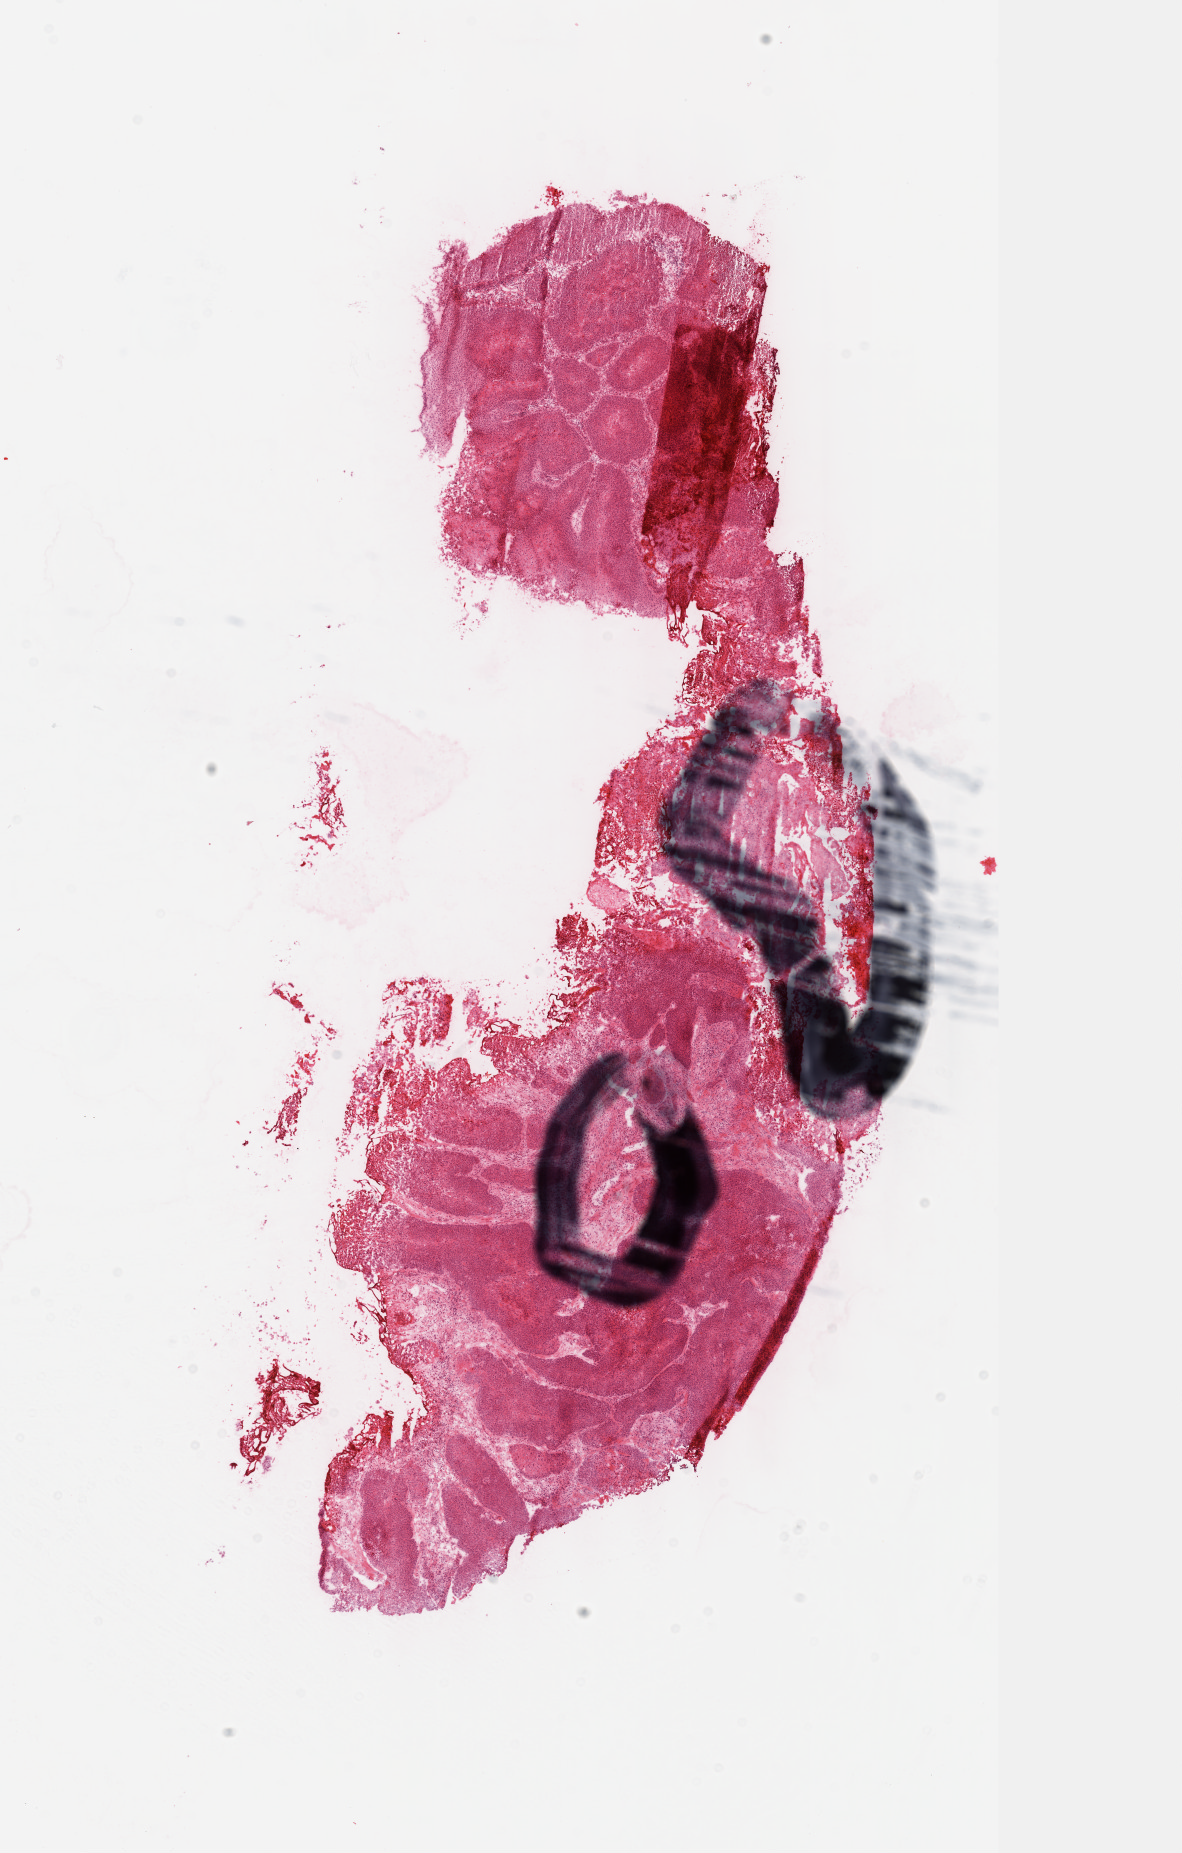
Digitized Hematoxylin and eosin (H&E) stained tissue section (whole slide) — whole scanned area (about 9.6 x 15.0 mm, from a 40x scan) shown as a low-resolution overview; frozen section; primary tumour sample from the bladder. Female, age 78 years at initial diagnosis. Histologic grade: high grade. Slide review estimates, as recorded: tumour cells 55%, tumour nuclei 85%, normal cells 0%, stromal cells 35%, necrosis 10%. Infiltration values recorded for this section: lymphocyte infiltration 8%, monocyte infiltration 0%, neutrophil infiltration 2%.
Diagnosis: Transitional cell carcinoma. AJCC pathologic stage: II (7th edition).